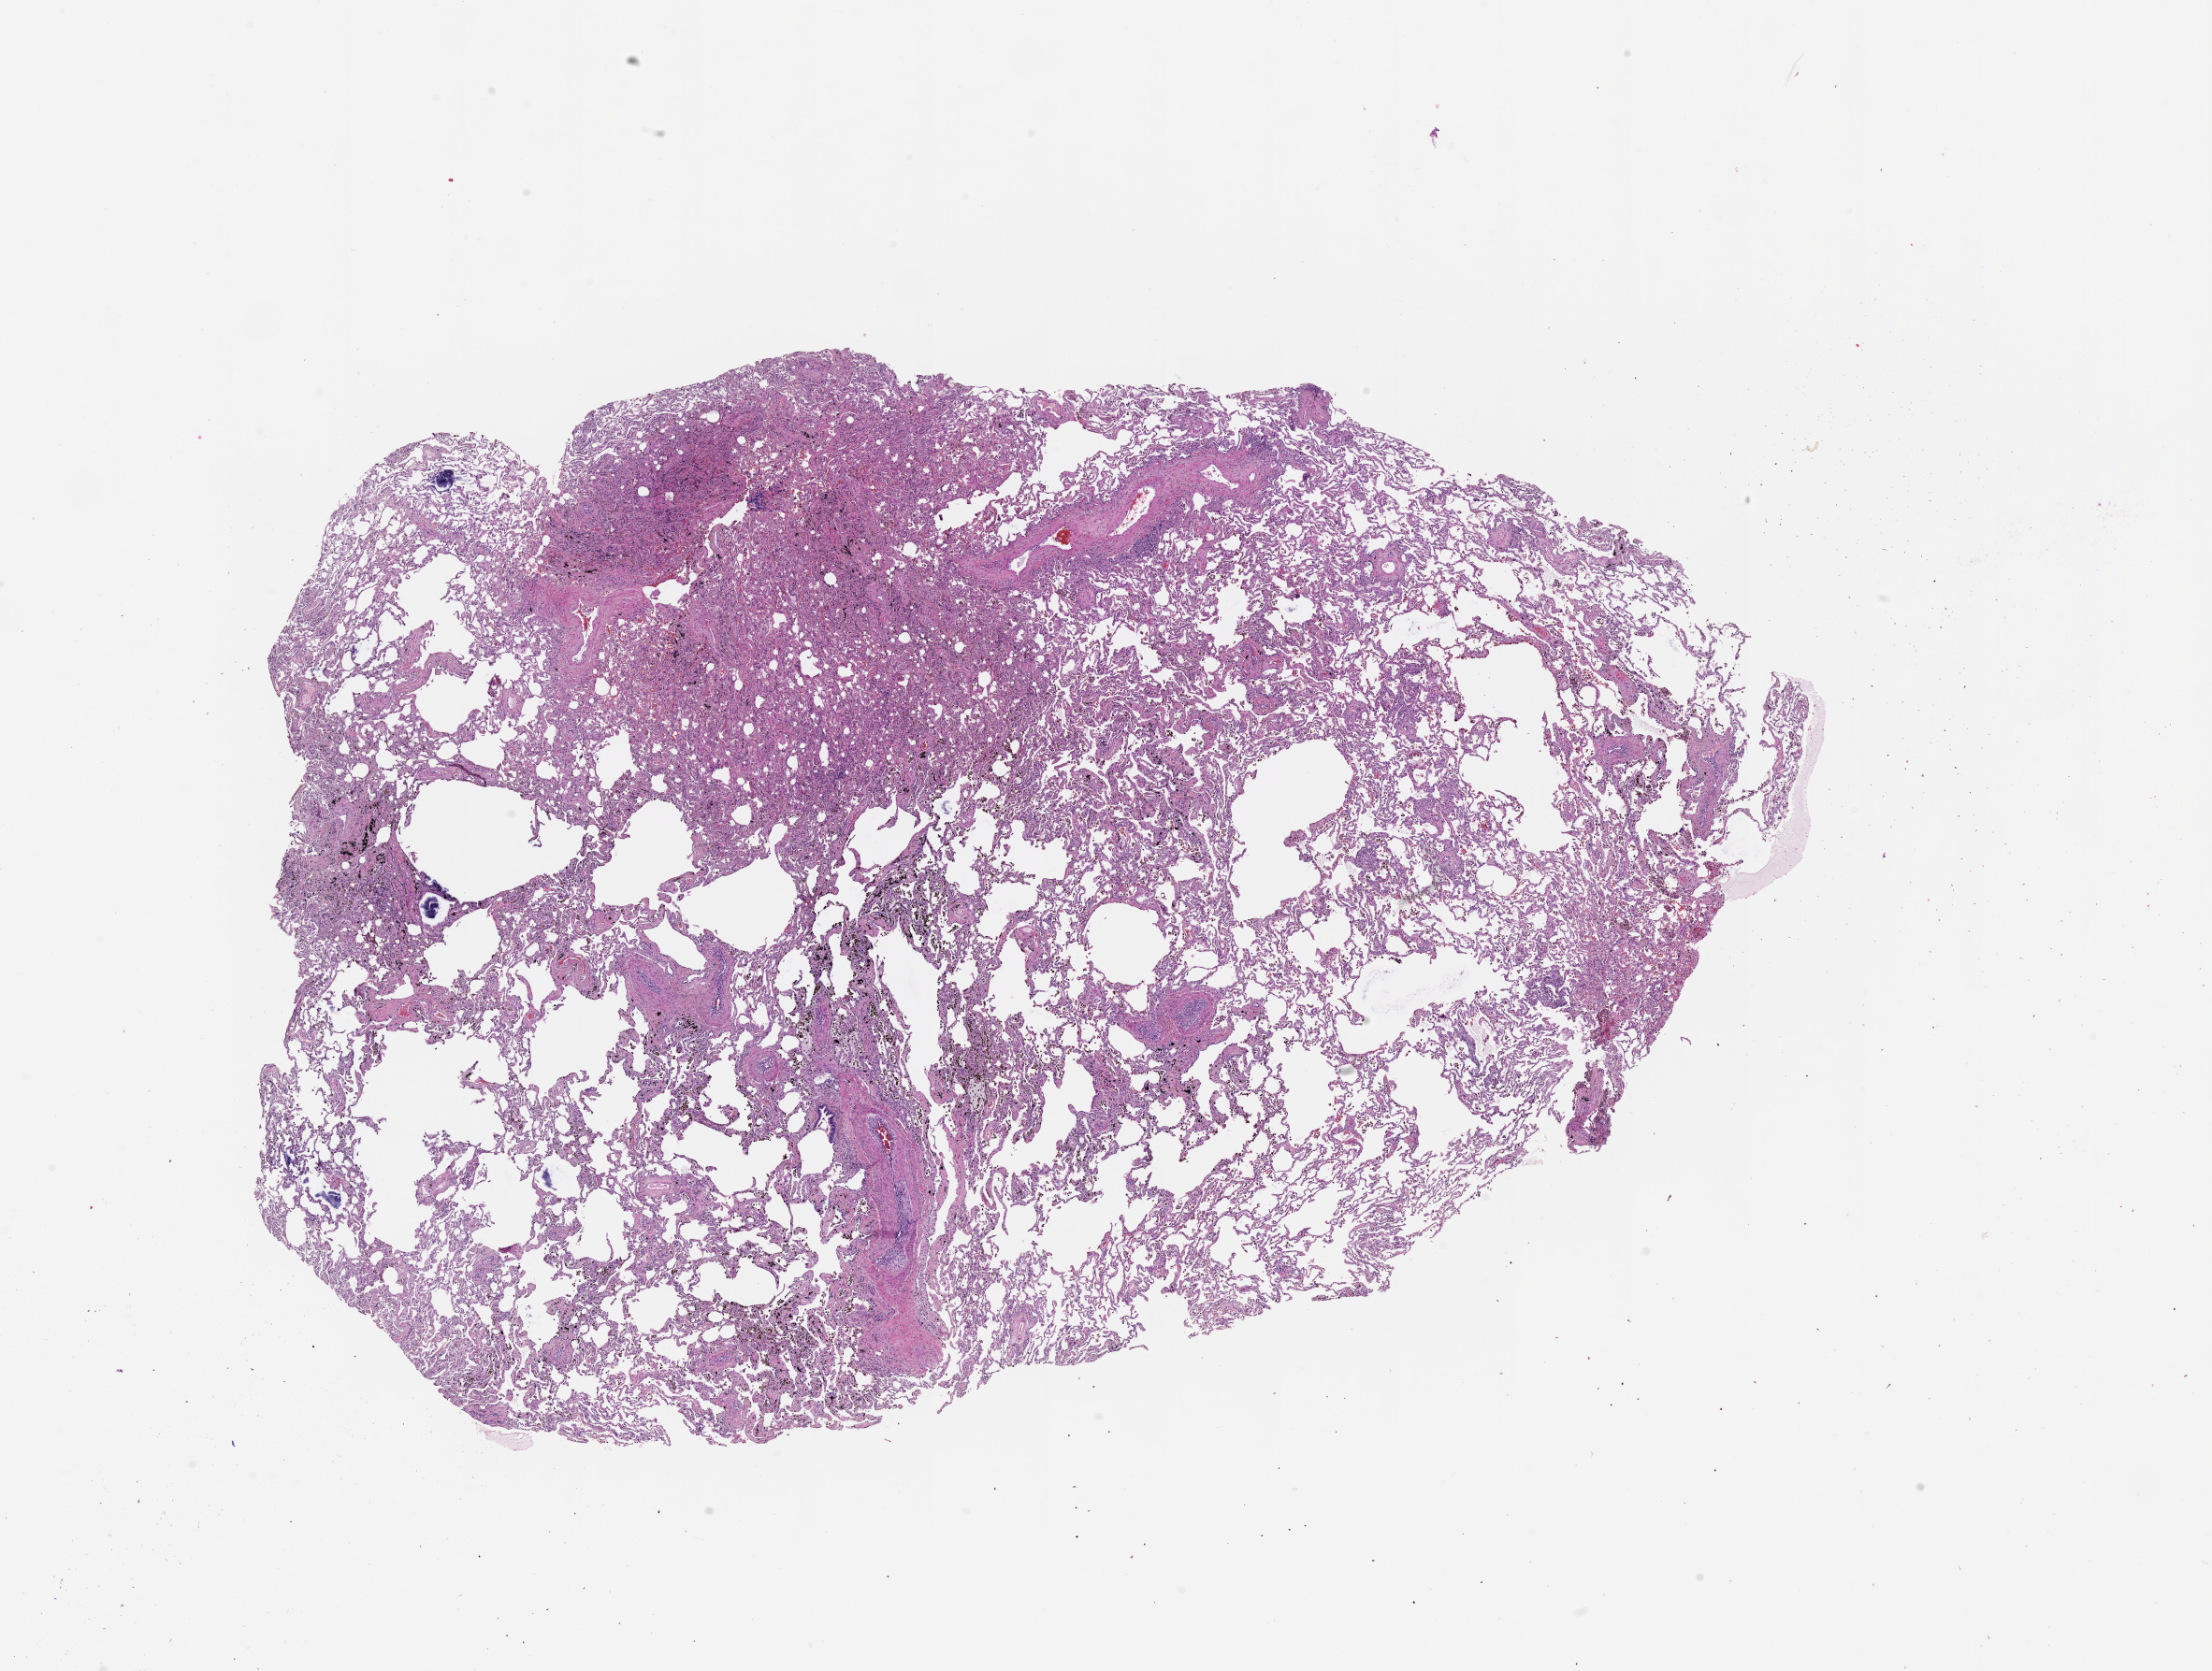
Whole-slide histology image, H&E-stained — whole scanned area (about 19.0 x 14.4 mm, acquisition: 20x scan) shown as a low-resolution overview; lung, normal (non-tumour) tissue. Patient: male, age 60 years.
This section: normal (non-tumour) tissue from the same patient. Patient diagnosis (cohort enrolment): squamous cell carcinoma (lung).